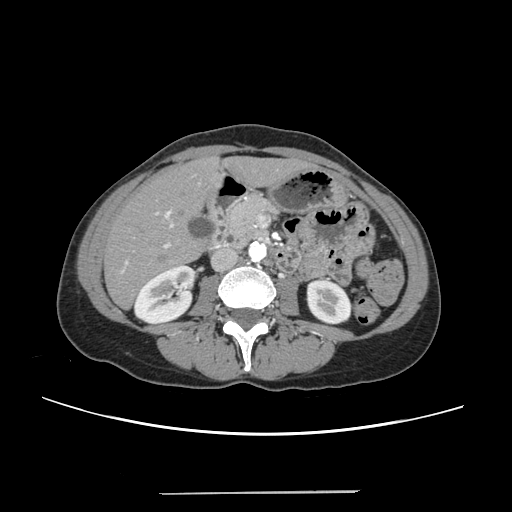
Contrast-enhanced abdominal CT, one axial slice; slice 96 of 240 in the series (ordered by position); 120 kVp; intravenous contrast given; soft-tissue window (W 400 / L 40 HU); 1.25 mm slice thickness; 512 × 512 image matrix. Female patient, age 60 years. Case-level facts recorded for this patient, not image findings: diagnosis: colorectal cancer liver metastases, imaged before liver resection; multiple liver metastases: no; largest metastasis: 1.5 cm.
Structures marked on this image (outlined manually by an expert reader):
- liver: box from (x=106, y=159) to (x=302, y=308) px
- planned liver remnant (the part of the liver to remain after resection): (x=106, y=160)–(x=302, y=307)
- portal vein (with intrahepatic branches): (x=122, y=210)–(x=173, y=271)